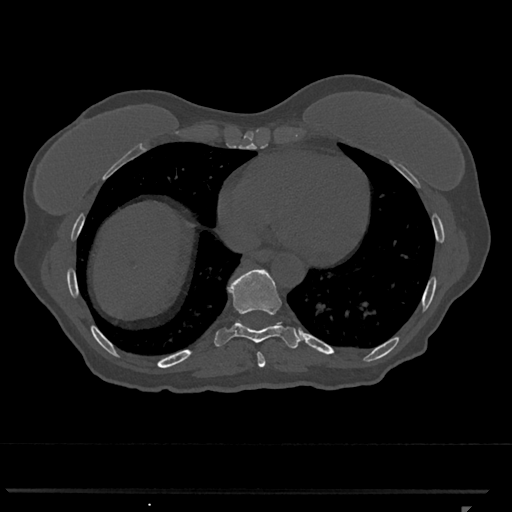
CT including the spine, one axial slice; slice 616 of 793 in the series (ordered by position); 120 kVp; bone window (W 1800 / L 400 HU); 512 × 512 image matrix, field of view 380 × 380 mm. Patient: female, 62 years. Case-level facts recorded for this patient, not image findings: primary cancer: renal.
Structures marked on this image (semi-automatic segmentation, software-assisted and operator-edited):
- T10 vertebra: box from (x=276, y=322) to (x=279, y=325) px
- T8 vertebra: (x=257, y=352)–(x=266, y=367)
- T9 vertebra: (x=214, y=269)–(x=300, y=349)